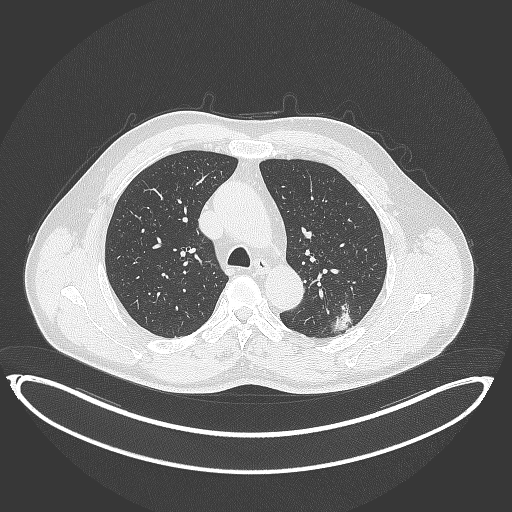
Chest CT, one axial slice. Slice 252 of 399 in the series (ordered by position). Reconstruction kernel B70f. Lung window (W 1500 / L -600 HU). 512 × 512 image matrix, field of view 469 × 469 mm. Patient: male, 58 years. From the clinical record (not read from this slice): clinical TNM (as recorded): T1c N0 M0; histopathological grade: G1-2.
Structures marked on this image (bounding box drawn by a radiologist):
- lung tumour (recorded histology: adenocarcinoma): box from (x=332, y=295) to (x=358, y=335) px